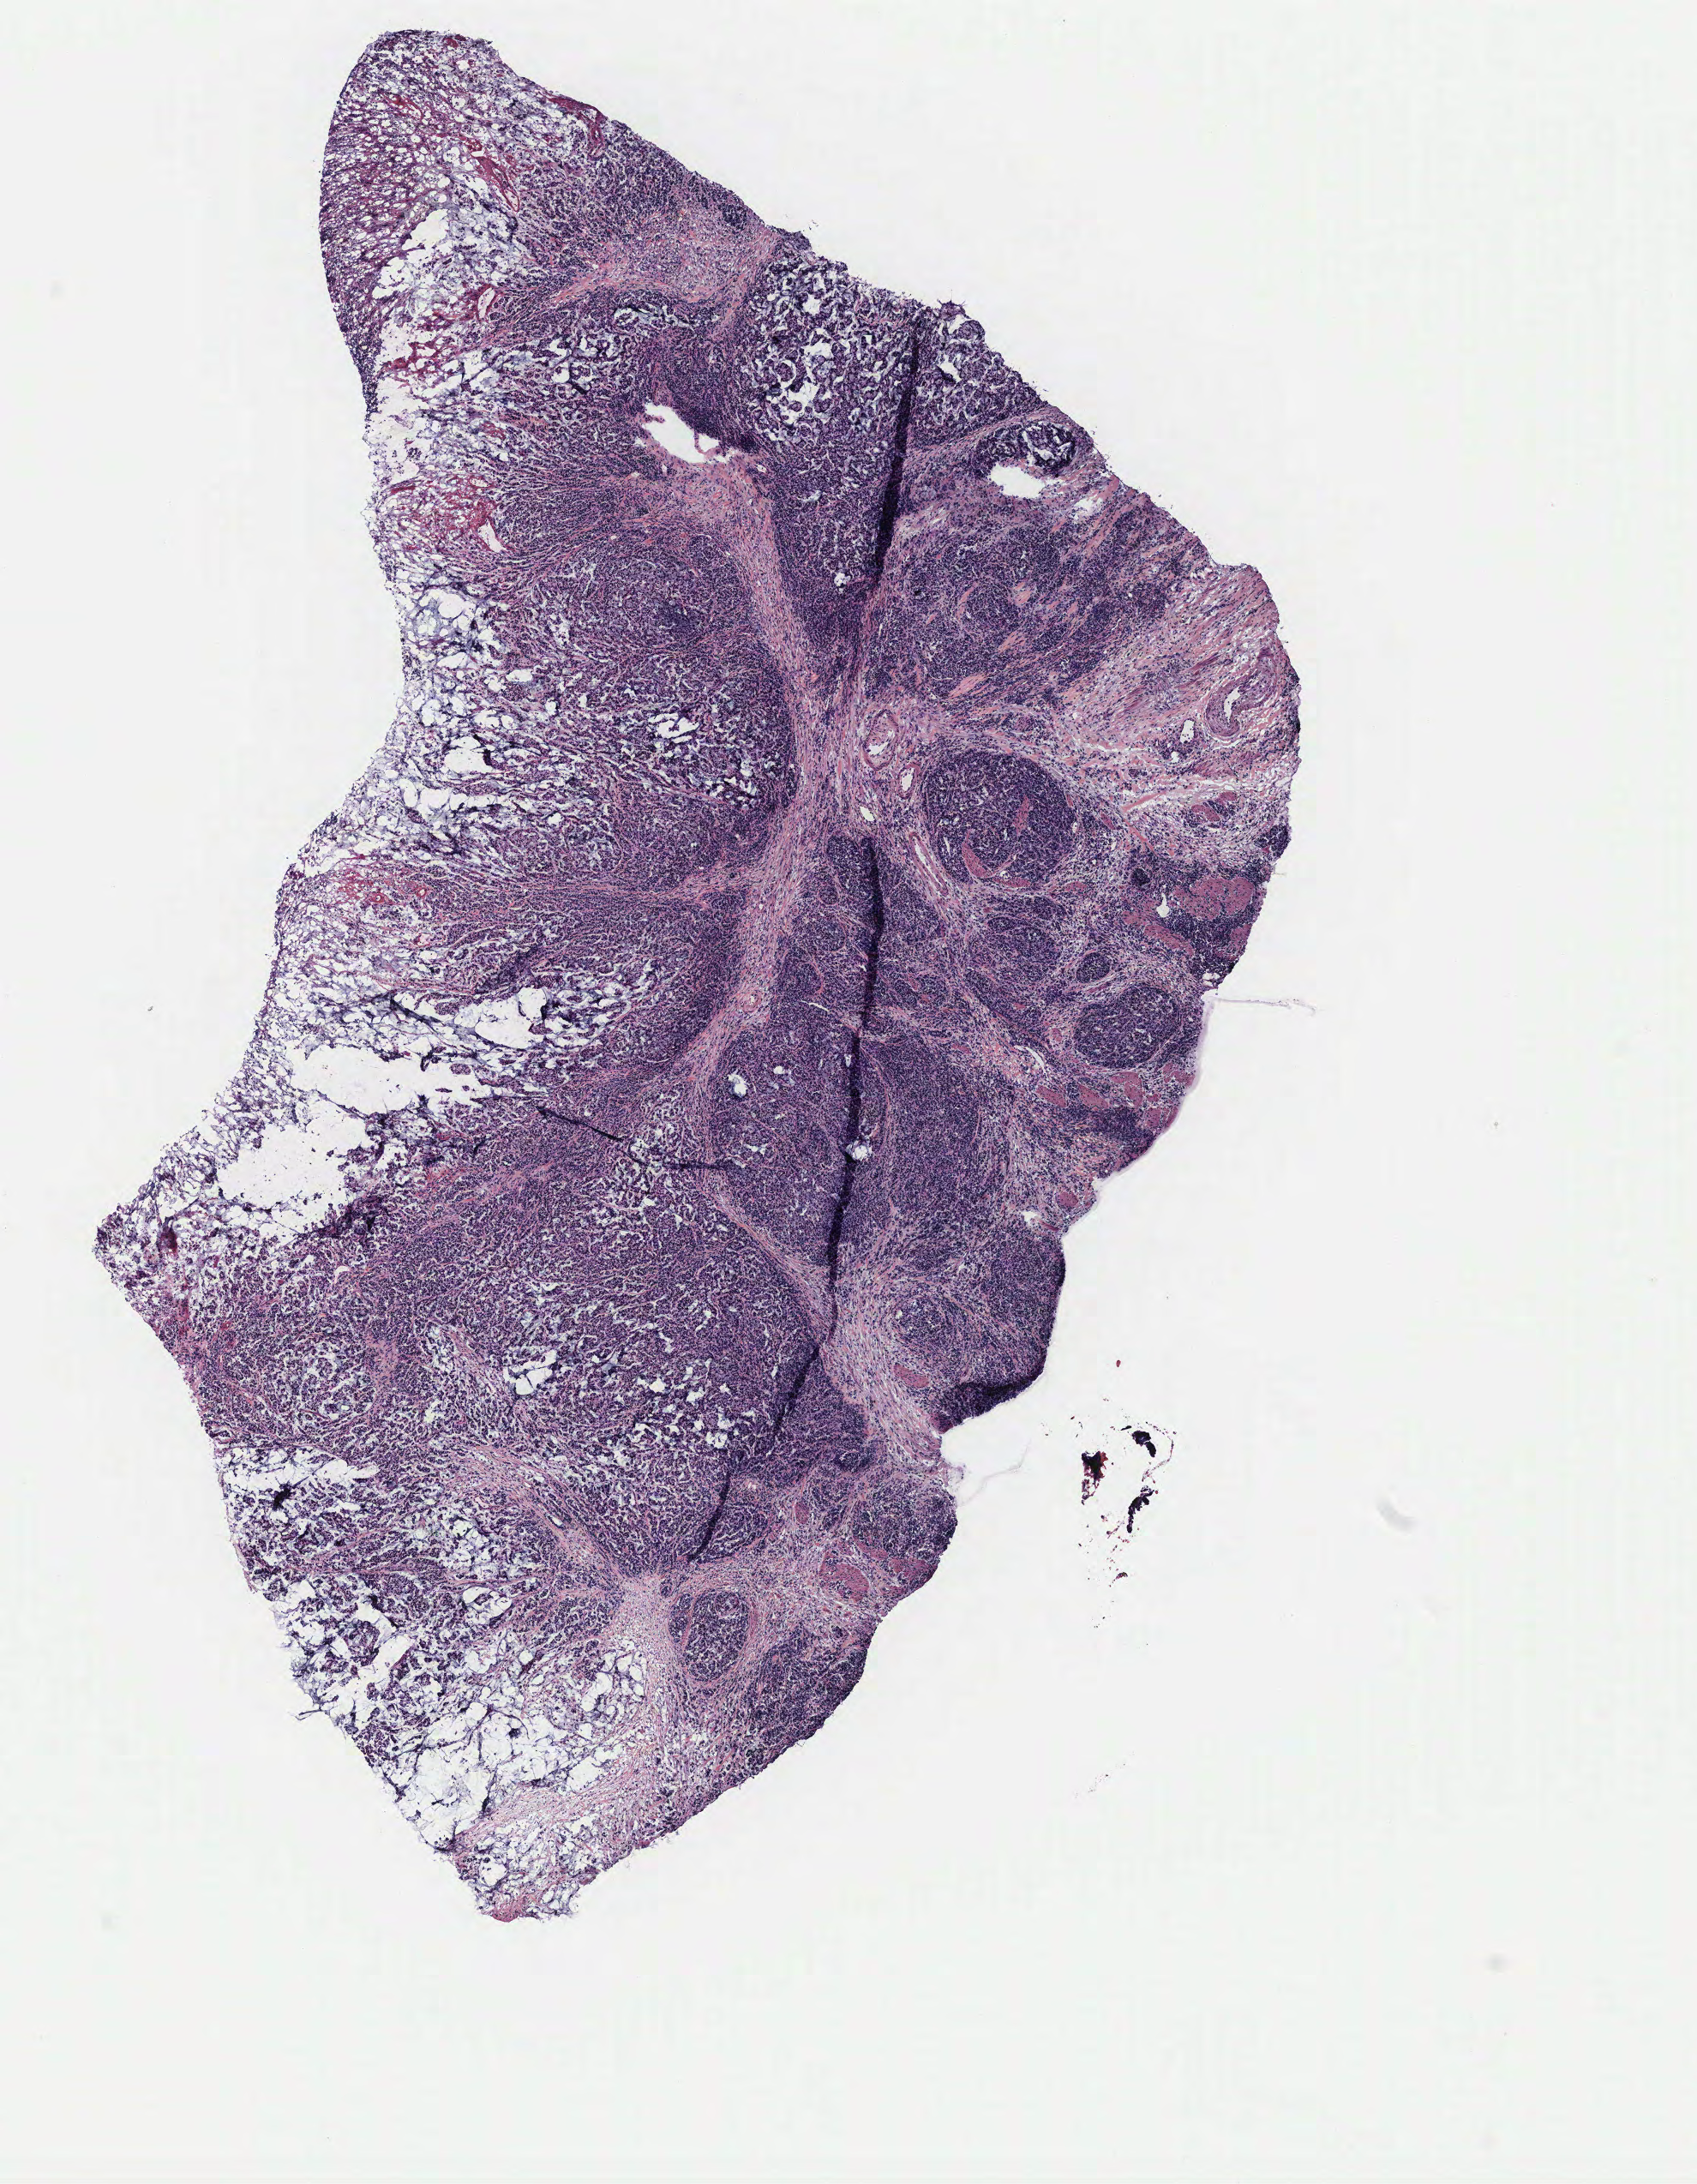
Digitized Hematoxylin and eosin (H&E) stained tissue section (whole slide), a low-resolution overview of the entire scanned area, about 7.9 x 10.2 mm (slide scanned at 40x); normal (non-tumour) tissue sample, colon. Patient: female, age 83 years.
This section: normal (non-tumour) tissue from the same patient. Patient diagnosis: Adenocarcinoma, NOS.